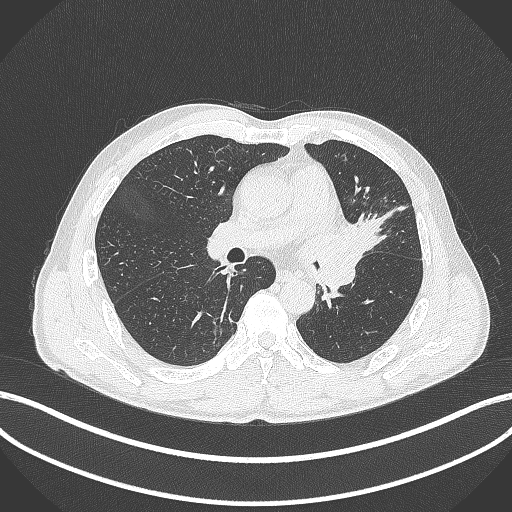
Chest CT, one axial slice; slice 234 of 429 in the series (ordered by position); reconstruction kernel B70f; 120 kVp; lung window (W 1500 / L -600 HU); 512 × 512 image matrix, field of view 400 × 400 mm. Male patient, age 57 years. Case-level facts recorded for this patient, not image findings: clinical TNM (as recorded): T2b N0 M0.
Structures marked on this image (rectangle marked by the reading radiologist):
- lung tumour (recorded histology: squamous cell carcinoma): box from (x=334, y=216) to (x=382, y=274) px